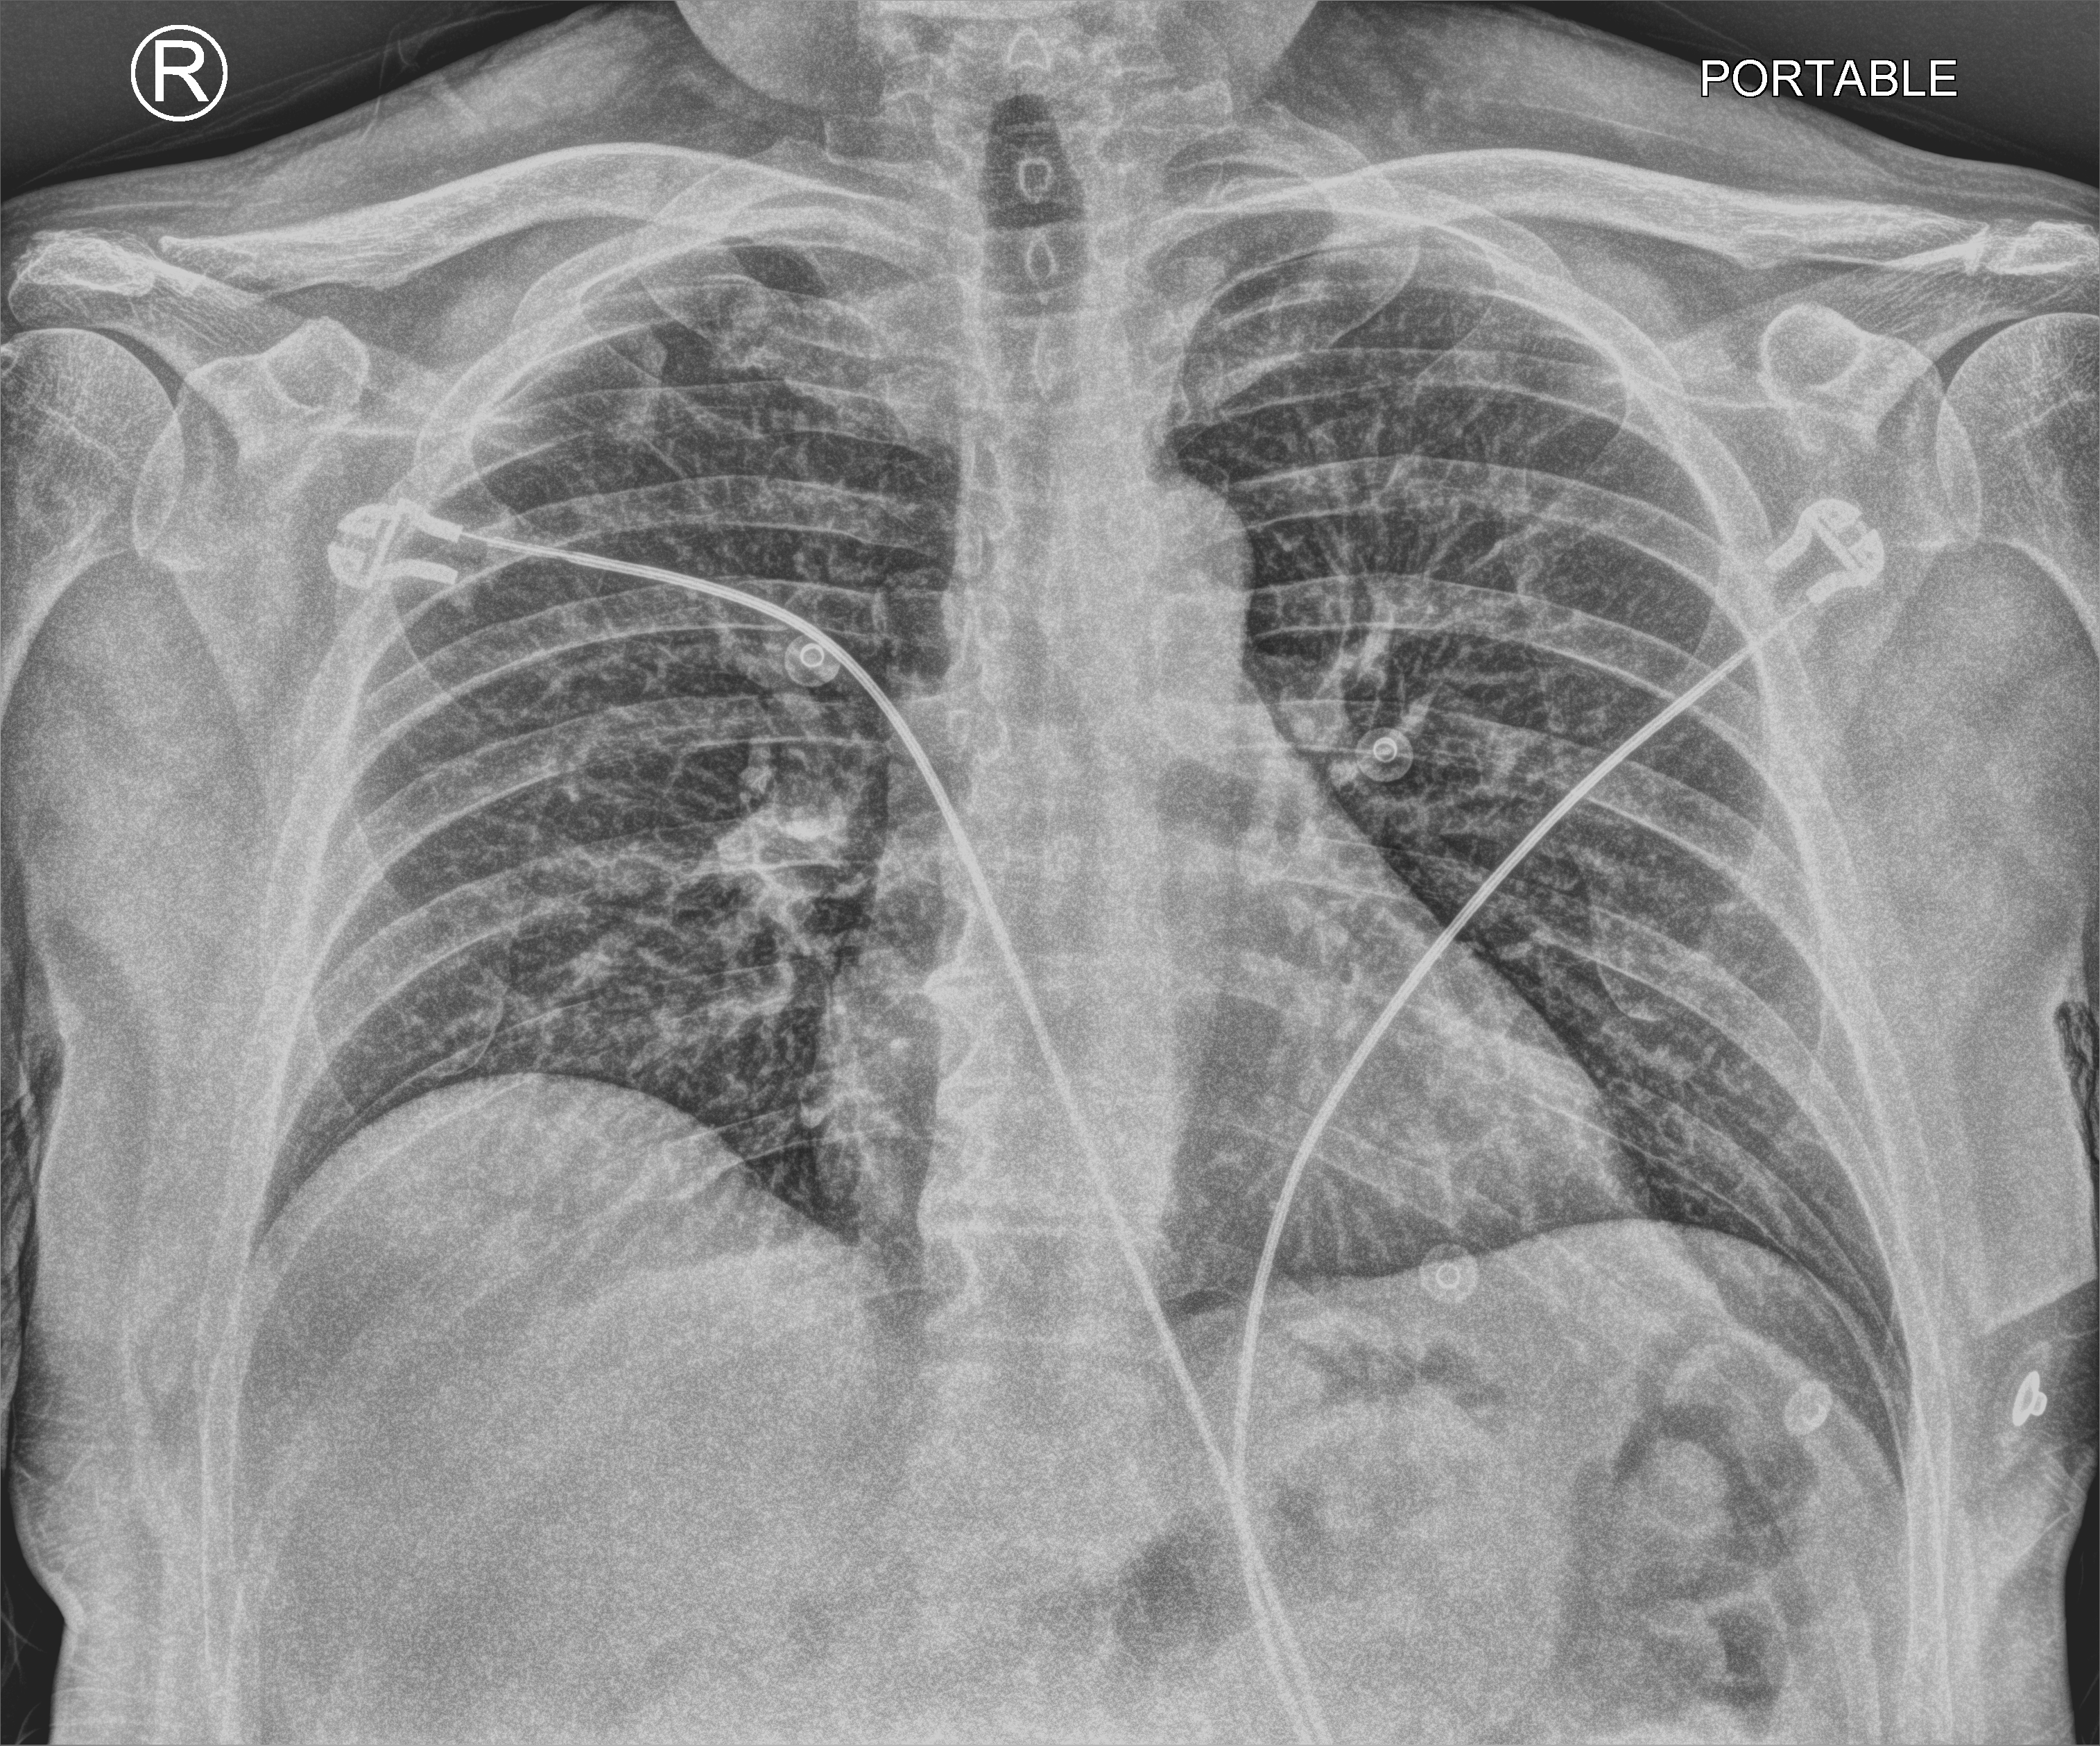
Bedside chest radiograph (computed radiography), anteroposterior (AP) projection. Male patient hospitalised with COVID-19, age 18–59 years.
From the hospital-stay record, not from the radiograph (when in the stay this image was taken is not recorded): admitted to intensive care during this hospital stay: no.